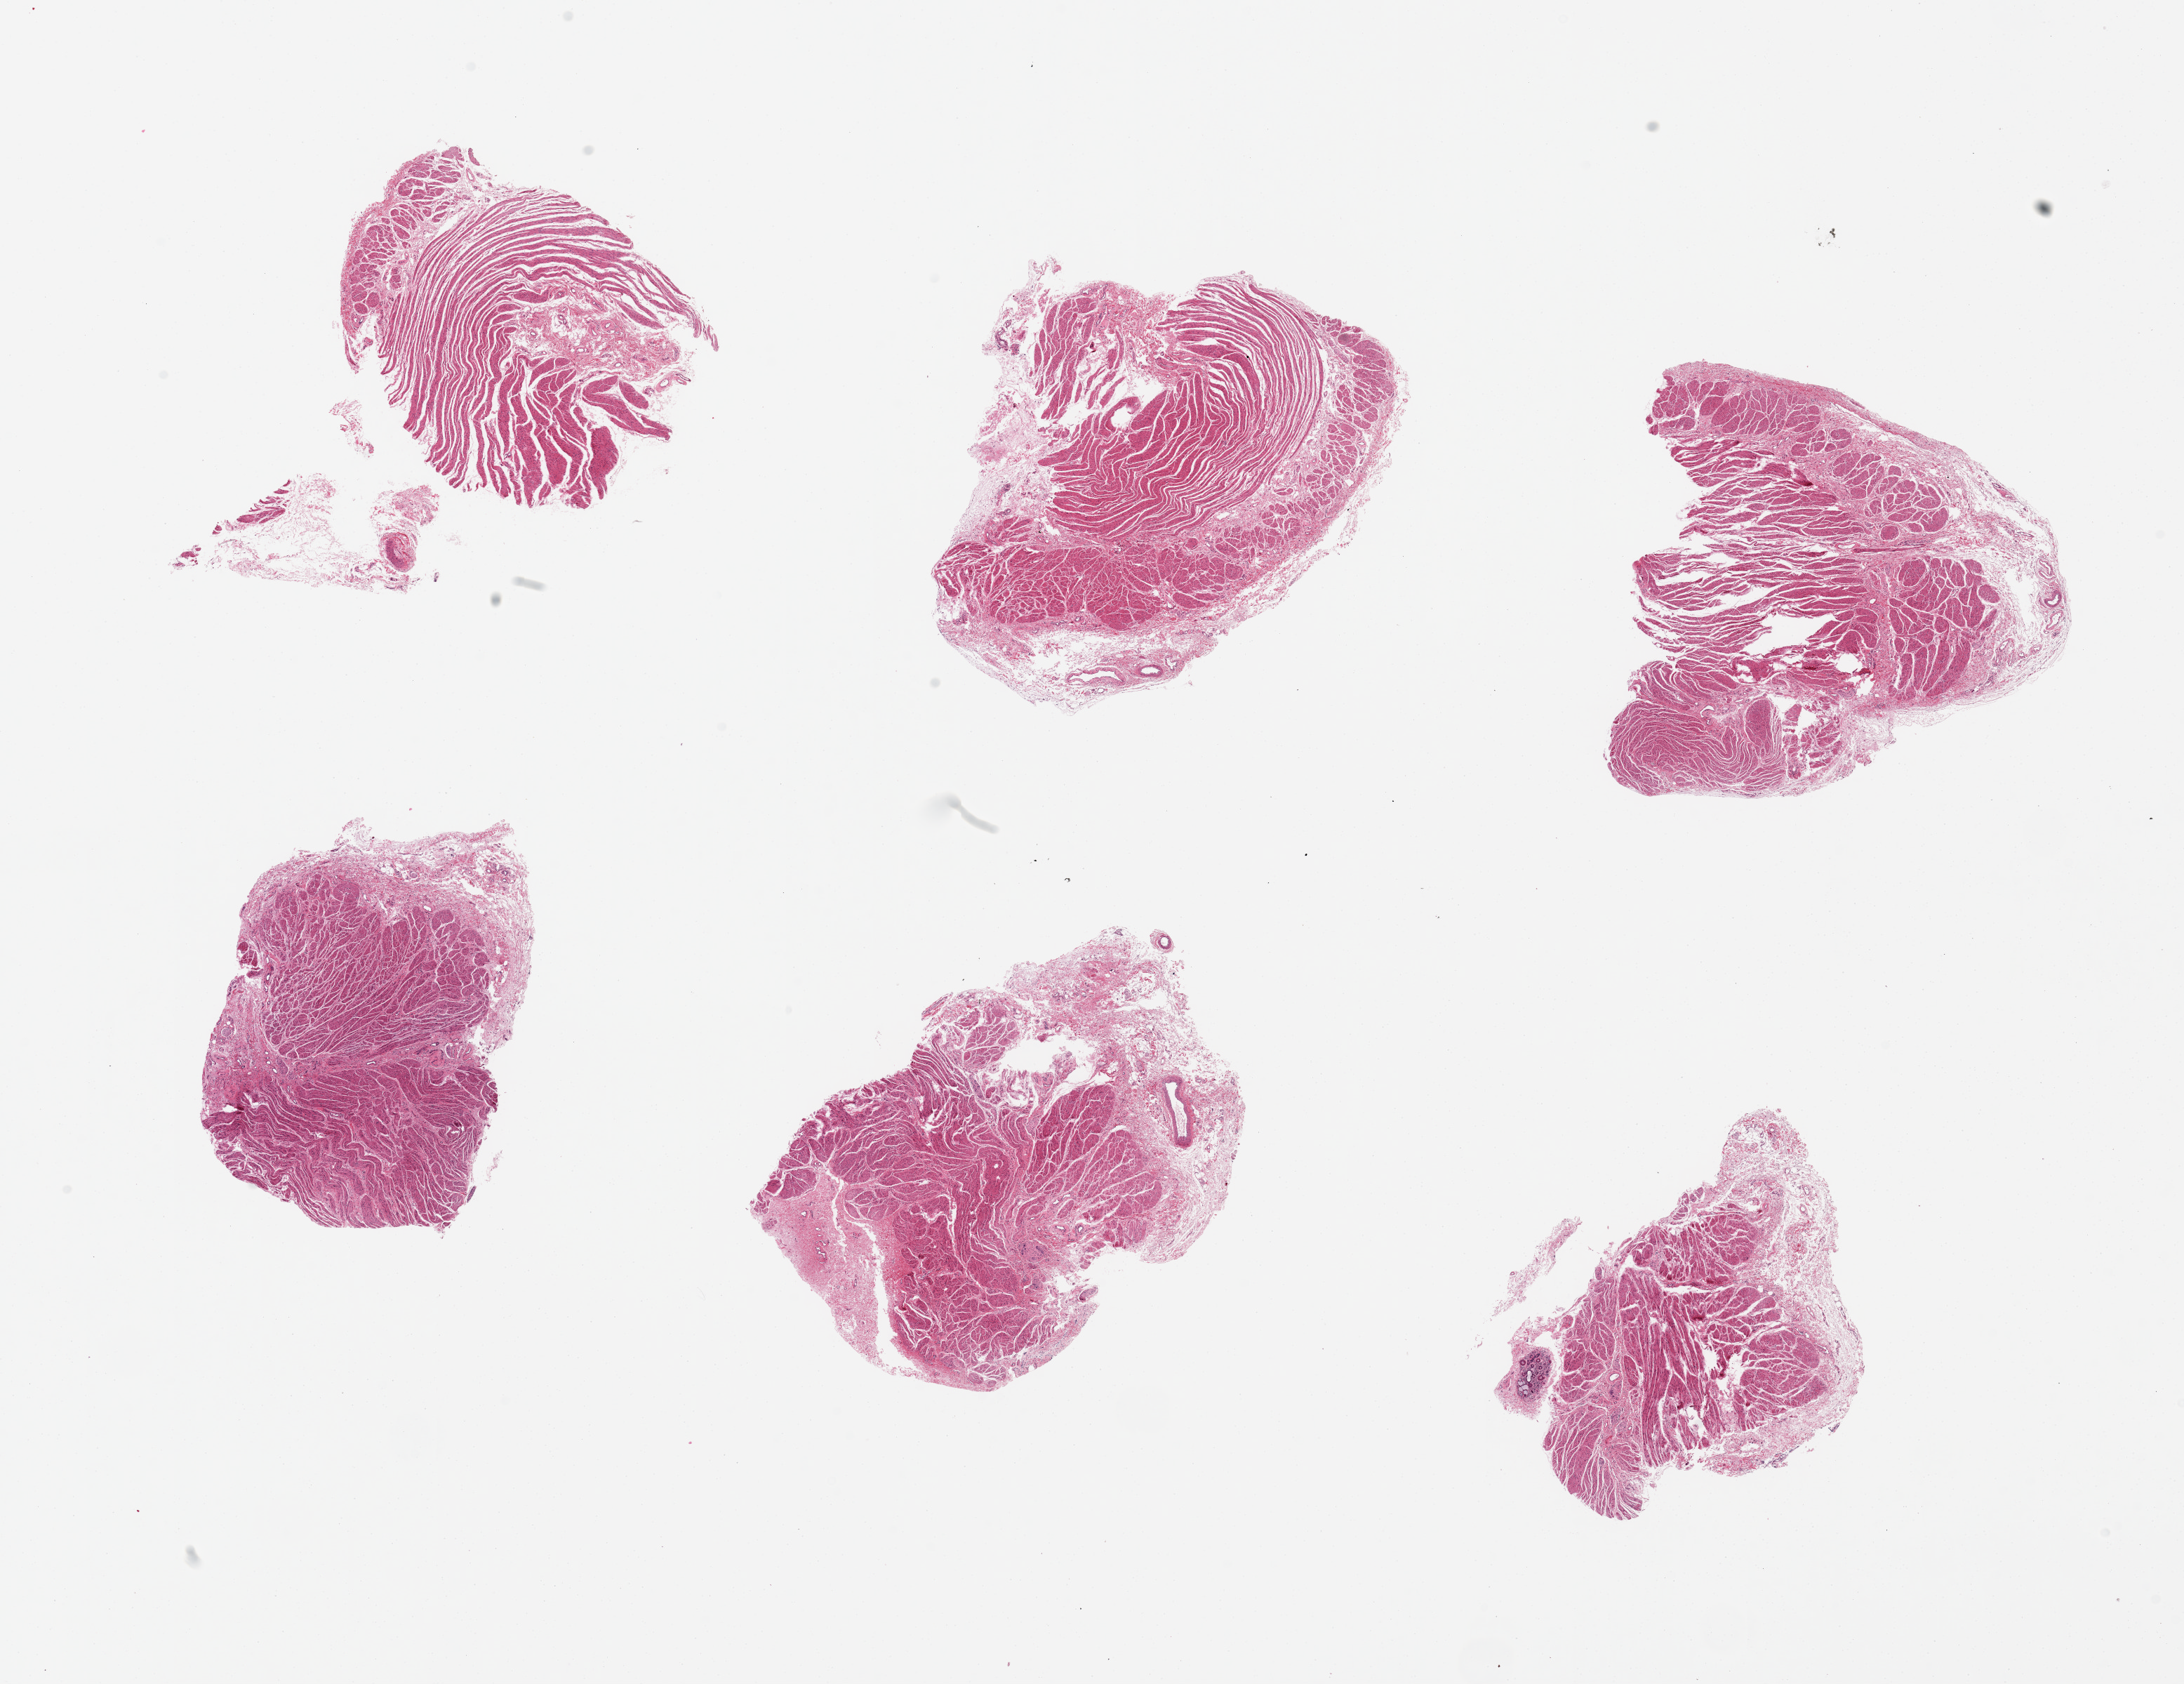
Digitized H&E-stained section, low-resolution overview of the scanned area, about 24.6 x 19.0 mm; PAXgene-fixed, paraffin-embedded tissue; section of gastroesophageal junction (target tissue); donor tissue sample. Donor sex: female.
Reviewer comment on this tissue sample: 6 pieces, up to 6x4.5mm; all muscularis, good specimens.